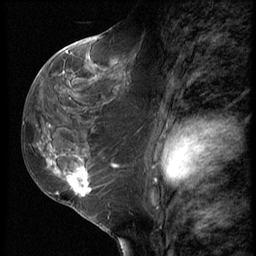
Breast MRI (dynamic contrast-enhanced), one sagittal slice. 3 images stored at this slice position (order not interpretable as contrast timing). 1.5 T. TE 4.2 ms, TR 9 ms. 2.5 mm slice thickness. 256 × 256 image matrix, field of view 180 × 180 mm. Female patient, age 50 years. From the clinical record (not read from this slice): setting: breast cancer imaged before/during neoadjuvant chemotherapy; receptor status: HR-positive, HER2-negative.
Structures marked on this image (semi-automatically segmented with operator editing):
- analysis volume of interest (the breast-tissue region the enhancement analysis was run in; not a lesion): bounding box (x1, y1, x2, y2) in pixels: (32, 91, 118, 209)
- tumour enhancement mask (voxels above the 140 % enhancement threshold inside the analysis volume of interest): (47, 158, 94, 196)